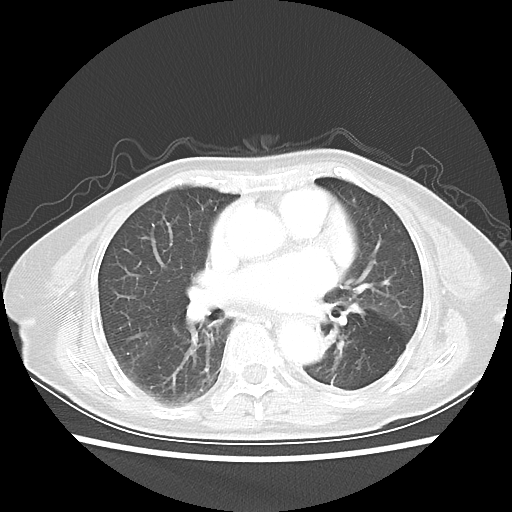
Chest CT, one axial slice. Position 25 of 50 along the scan axis. Lung window (W 1500 / L -600 HU). 512 × 512 image matrix, field of view 335 × 335 mm. Female patient, age 81 years. Case-level facts recorded for this patient, not image findings: clinical TNM (as recorded): T2 N0 M1a.
Structures marked on this image (rectangle marked by the reading radiologist):
- lung tumour (recorded histology: squamous cell carcinoma): box from (x=305, y=315) to (x=346, y=371) px